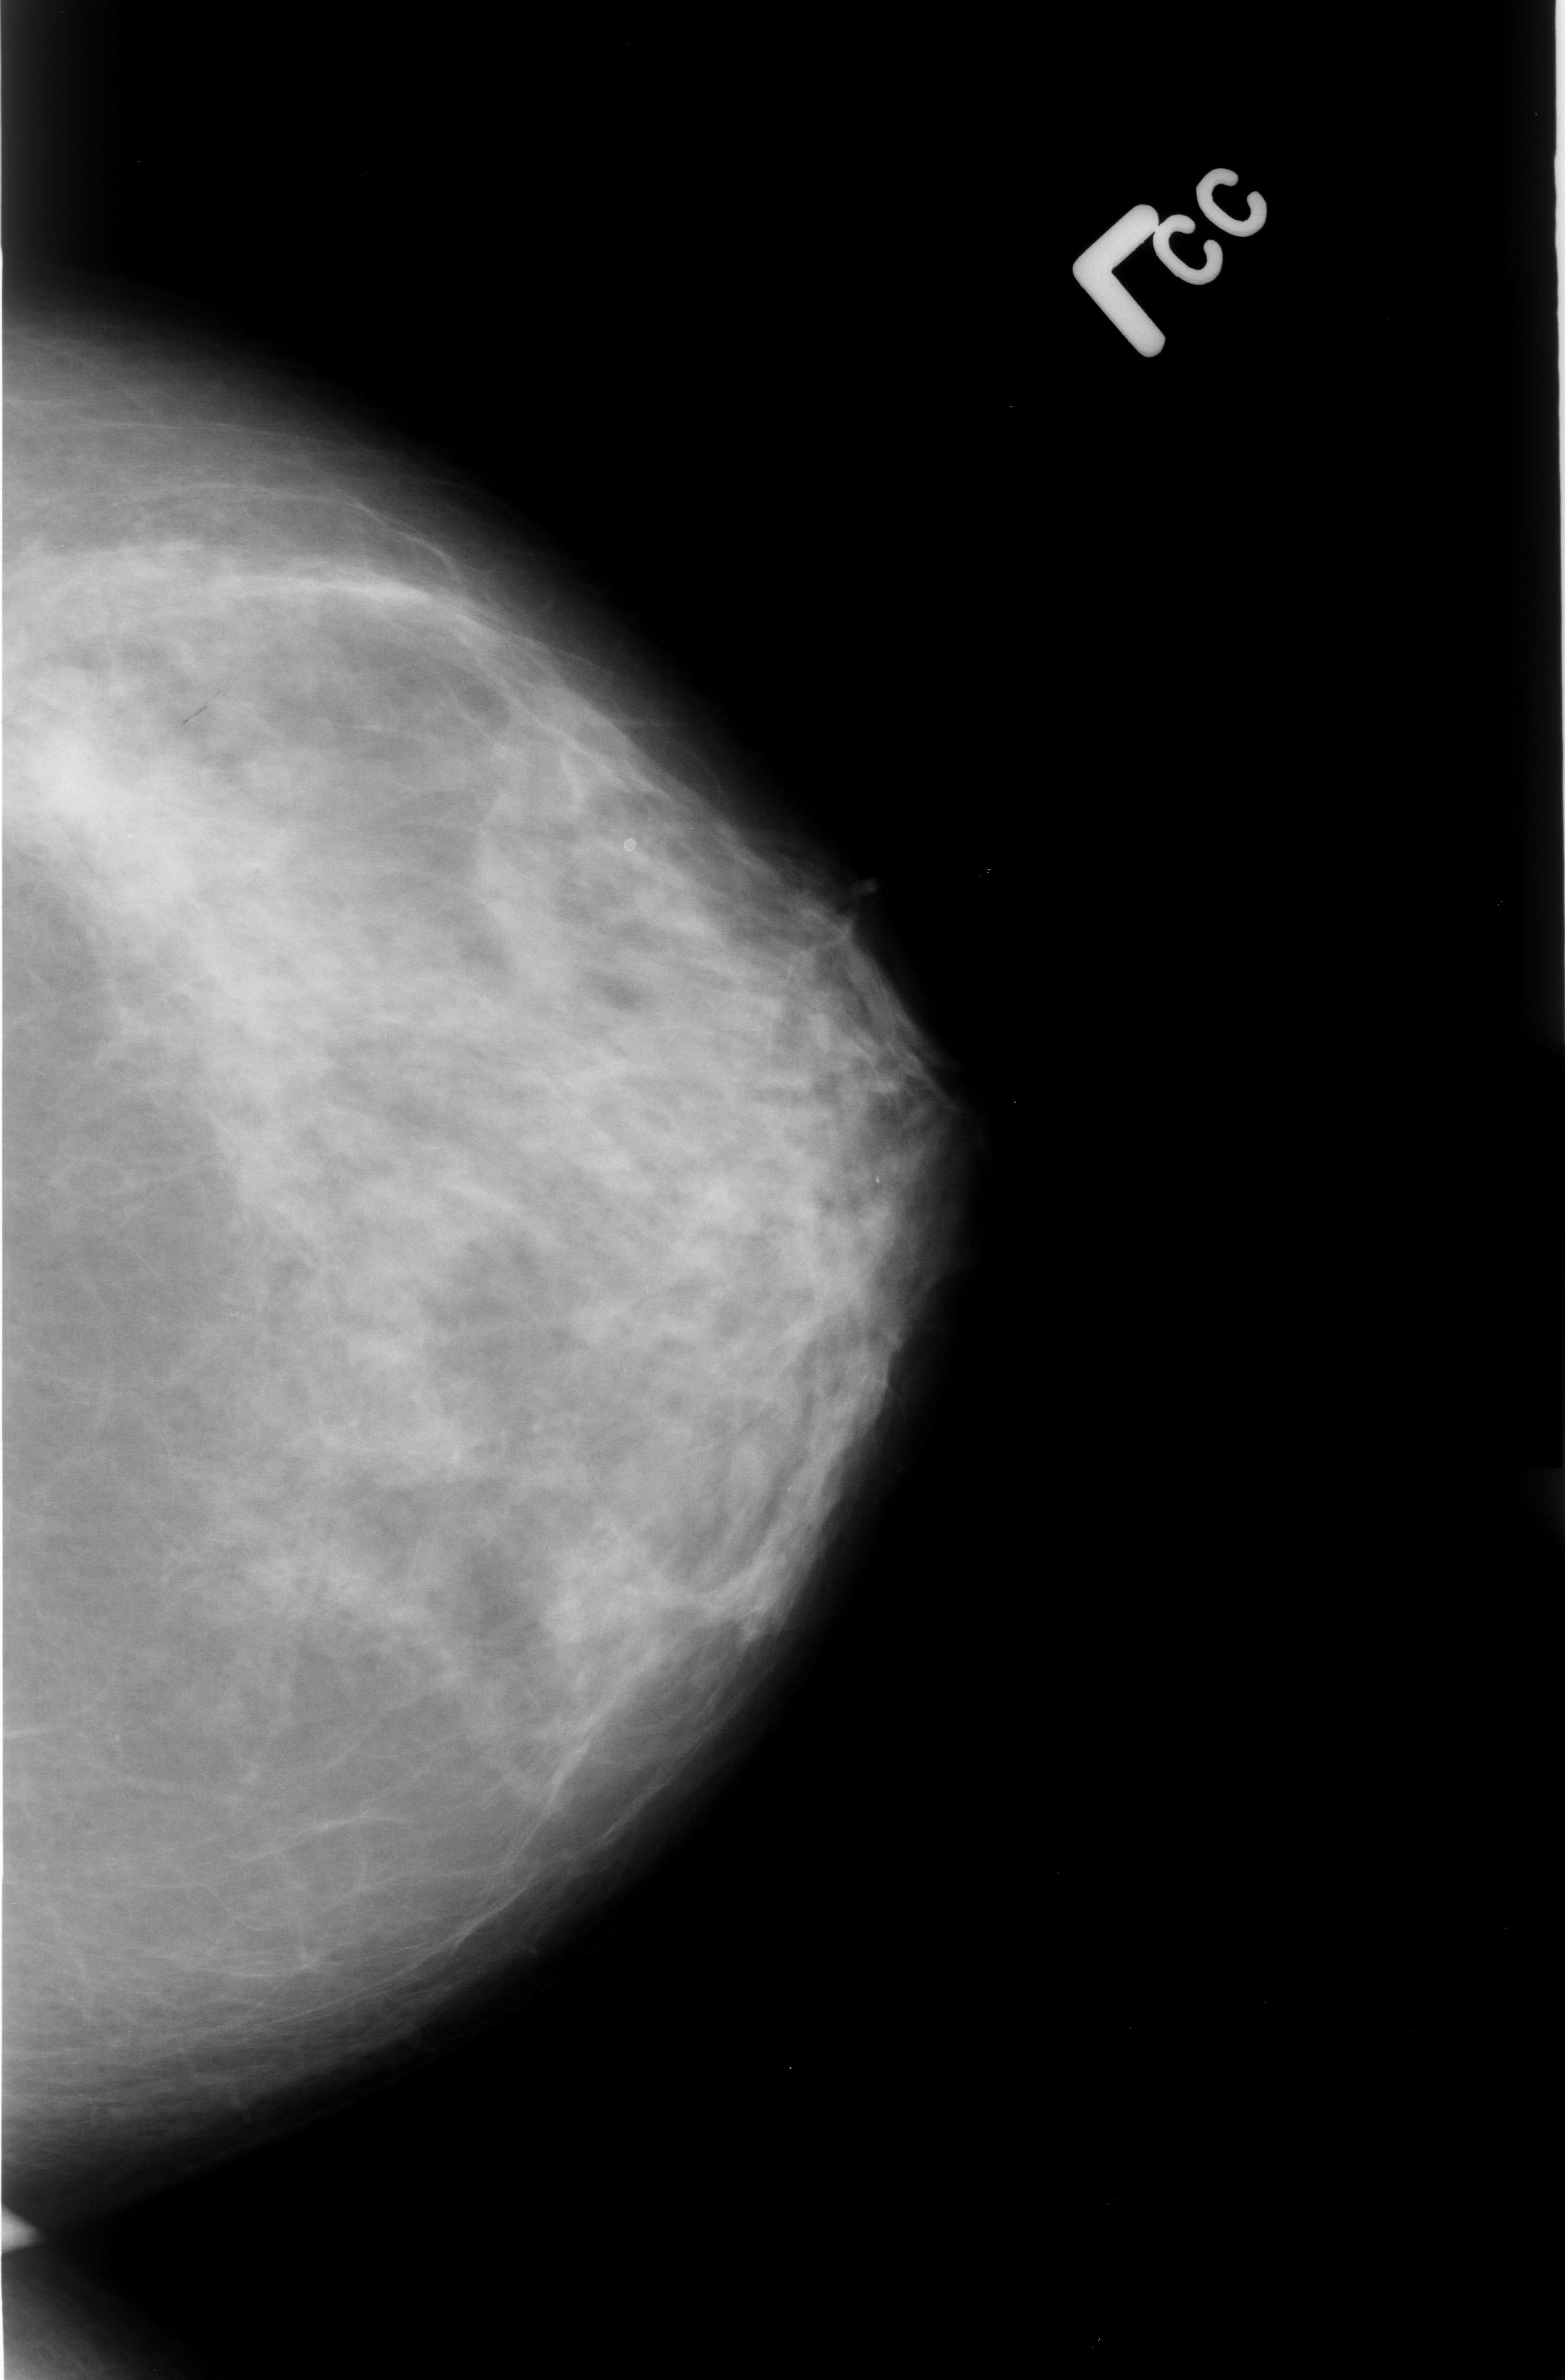
Mammogram (digitized film); left breast; CC view; breast composition: heterogeneously dense (BI-RADS density category 3 of 4); 1565 × 2380 image matrix.
Expert-marked regions of interest on this film, with their recorded descriptors:
- mass, shape irregular / architectural distortion, margins ill defined / spiculated; BI-RADS assessment category 4; pathology result (as recorded, not read from the image): malignant: bounding box (x1, y1, x2, y2) in pixels: (0, 687, 155, 876)